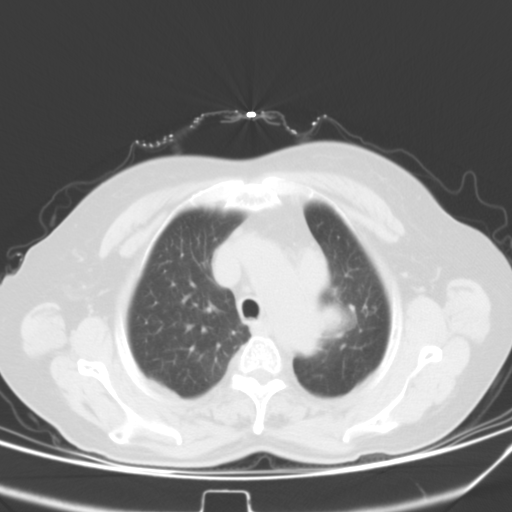
Chest CT, one axial slice. Slice 35 of 42 in the series (ordered by position). 120 kVp. Lung window (W 1500 / L -600 HU). 512 × 512 image matrix. Female patient, age 59 years. From the clinical record (not read from this slice): clinical TNM (as recorded): T3 N1 M0; histopathological grade: G3.
Annotated regions visible in this slice (bounding box drawn by a radiologist):
- lung tumour (recorded histology: small cell carcinoma): bounding box <319,298,337,336> (left, top, right, bottom; pixels)